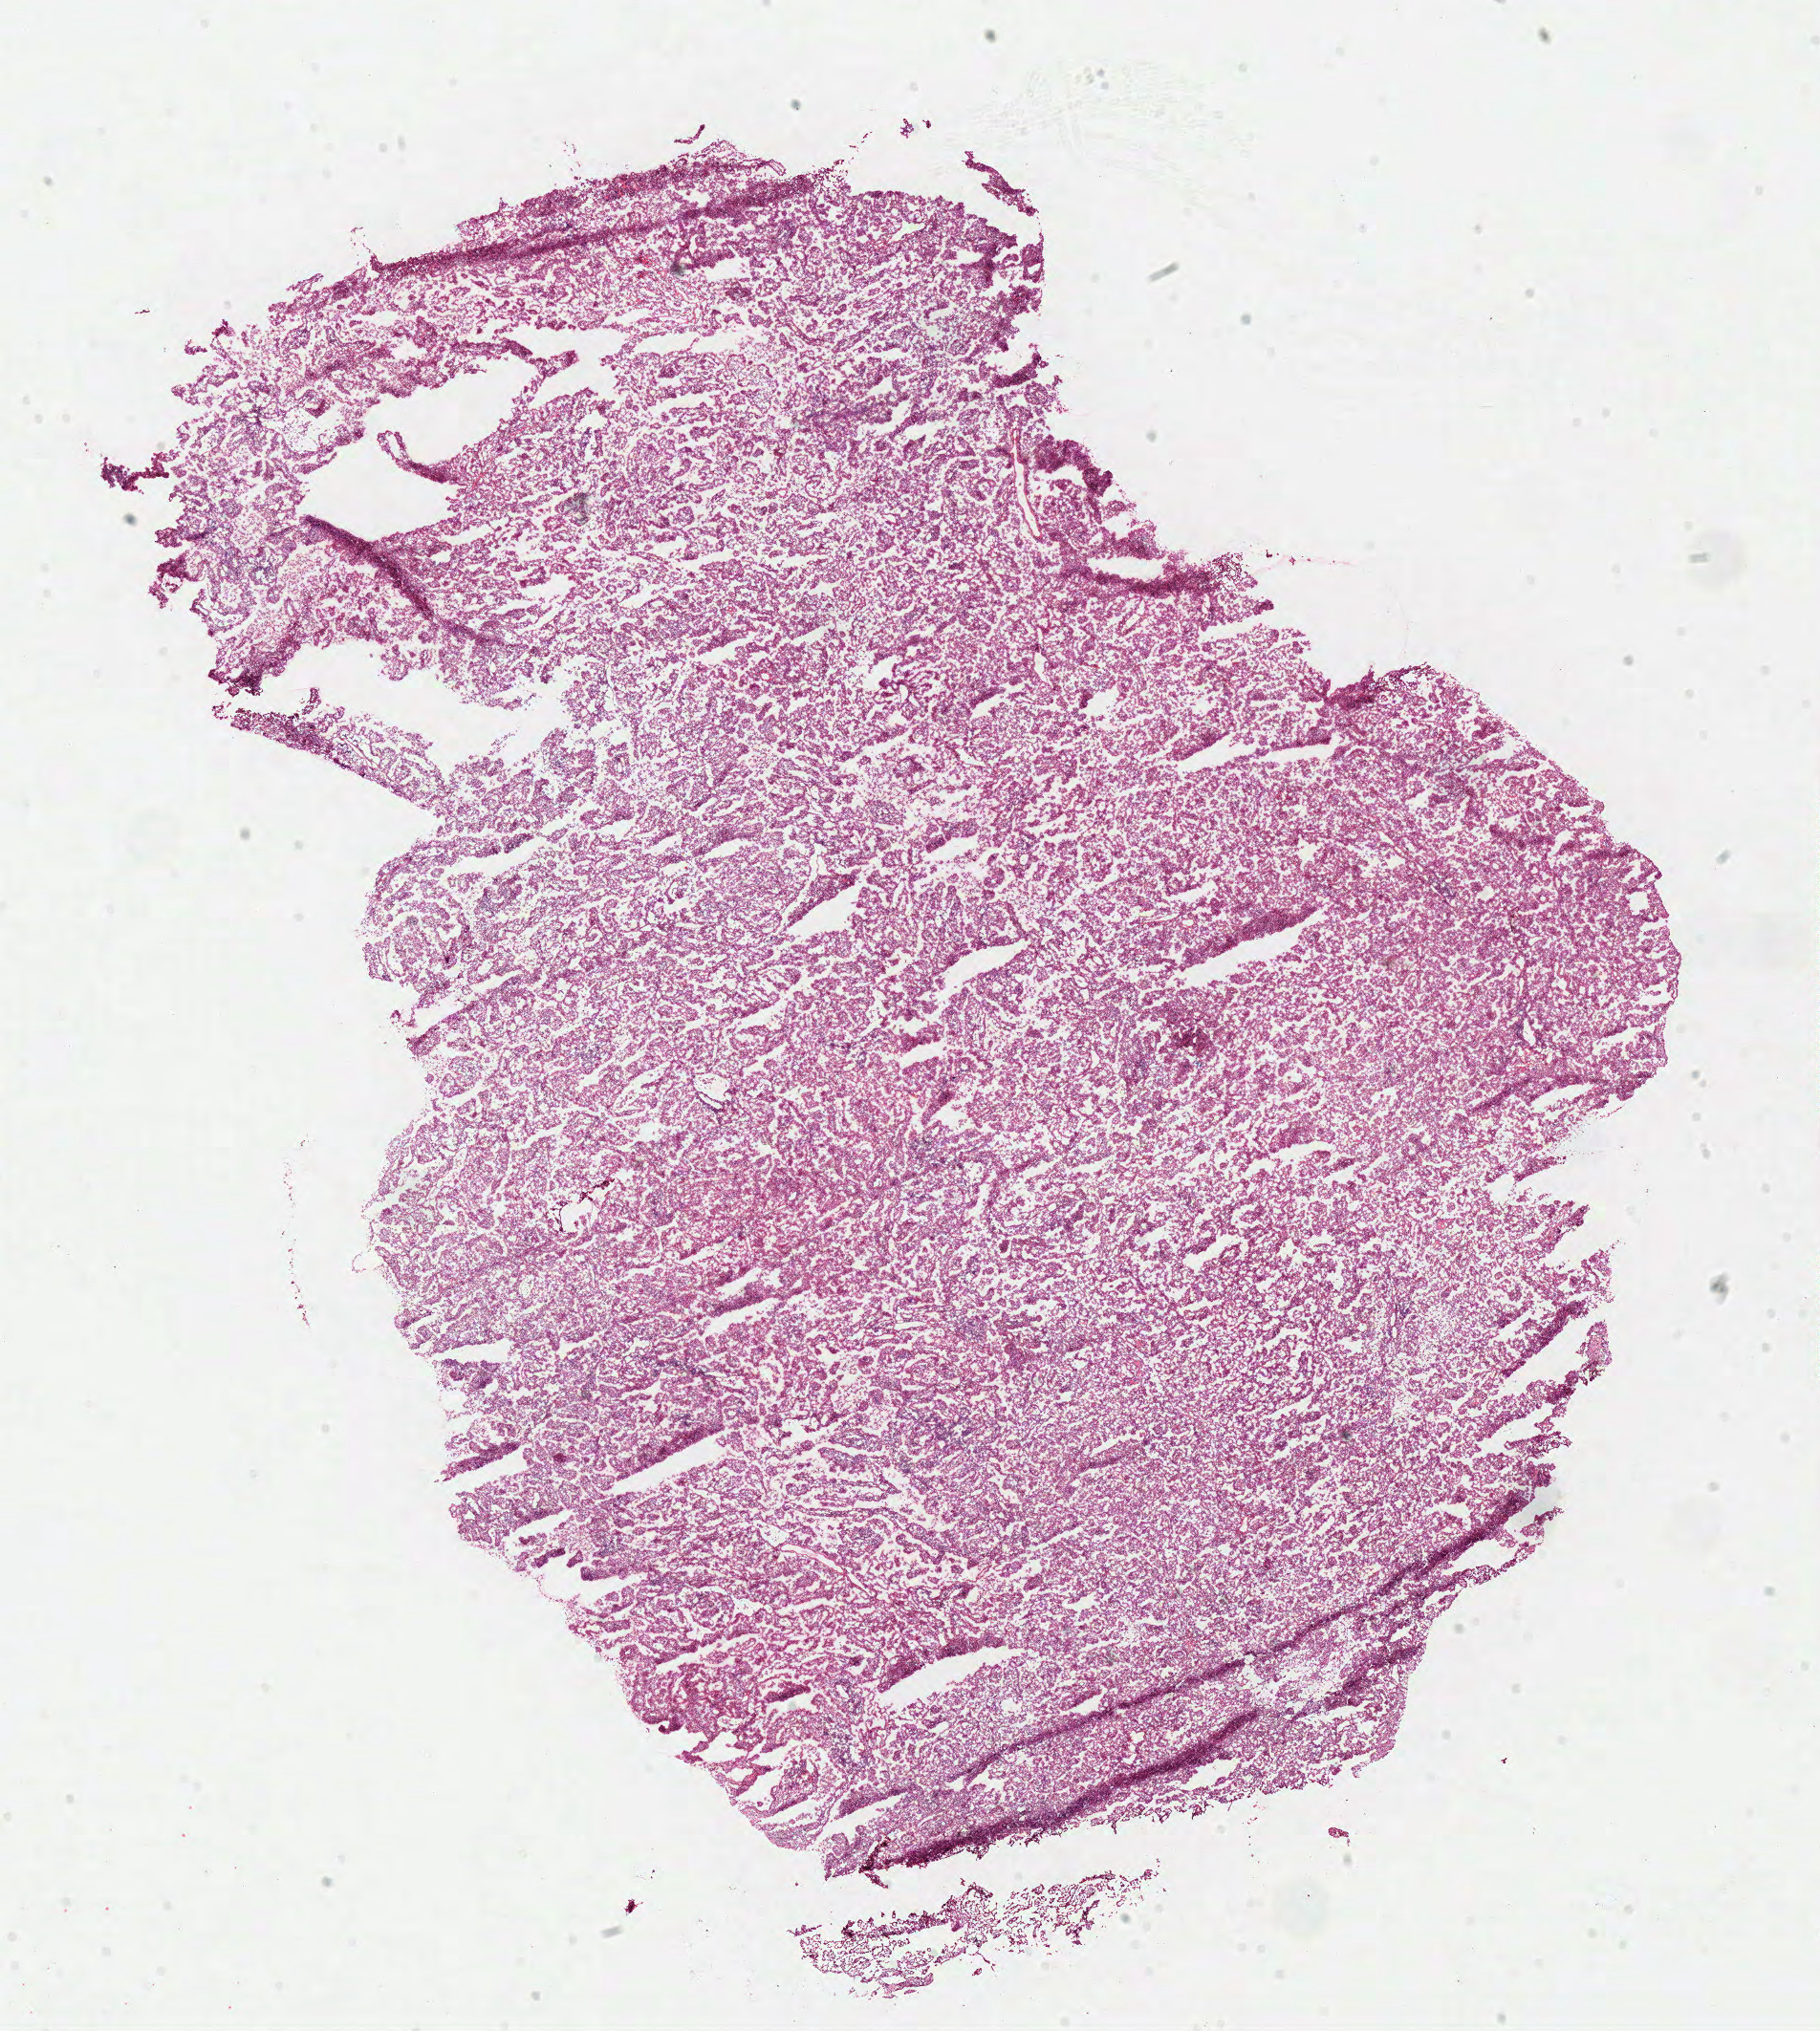
Whole-slide histology image, Hematoxylin and eosin (H&E) stained — shown as a low-resolution overview of the whole scanned area (about 15.0 x 16.7 mm, from a 40x scan). Frozen section. Primary tumour sample from the kidney. Patient: female, age at initial diagnosis 74 years. Pathologist review of this section (percent, as recorded): tumour cells 90%, tumour nuclei 85%, normal cells 0%, stromal cells 5%, necrosis 5%.
AJCC pathologic stage: I. Lymph nodes positive (case pathology): 0 of 2 examined. Pathologic diagnosis: Papillary adenocarcinoma, NOS. Laterality: right.